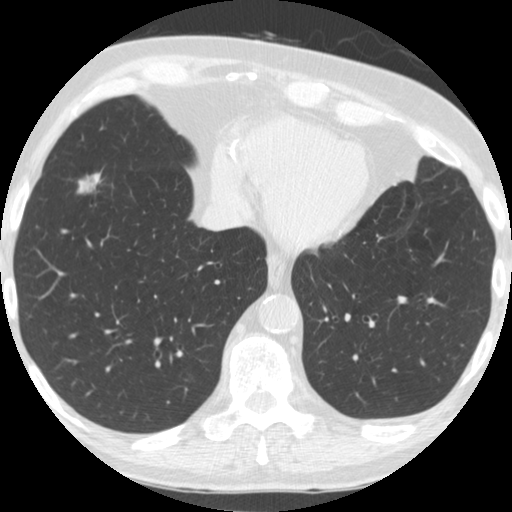
Low-dose screening chest CT, one axial slice. Position 64 of 182 along the scan axis. 120 kVp. Lung window (W 1500 / L -600 HU). 2.5 mm slice thickness. 512 × 512 image matrix.
Outlined on this slice (outlined manually by an expert reader):
- lesion 1 (tumor, lower lobe of right lung): bounding box [x1, y1, x2, y2] px = [77, 173, 101, 194]